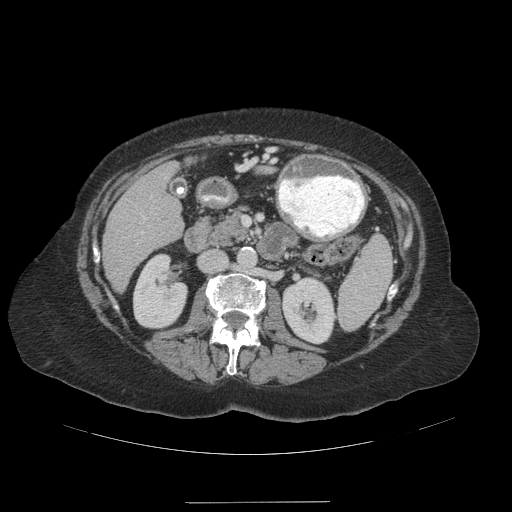
Contrast-enhanced abdominal CT (liver protocol), one axial slice; reconstruction kernel STANDARD; 140 kVp; soft-tissue window (W 400 / L 40 HU); 2.5 mm slice thickness; 512 × 512 image matrix, field of view 440 × 440 mm. Case-level facts recorded for this patient, not image findings: diagnosis: hepatocellular carcinoma (patient treated with transarterial chemoembolisation; whether this scan precedes or follows treatment is not stated here); TNM stage (as recorded): Stage-IVA; Child-Pugh class: A.
Outlined on this slice (semi-automatically segmented with operator editing):
- liver parenchyma outside the tumour (the mass and vessels are separate outlines, so this box may not span the whole liver): bounding box [x1, y1, x2, y2] px = [102, 162, 184, 292]
- liver vessels: [141, 216, 146, 234]